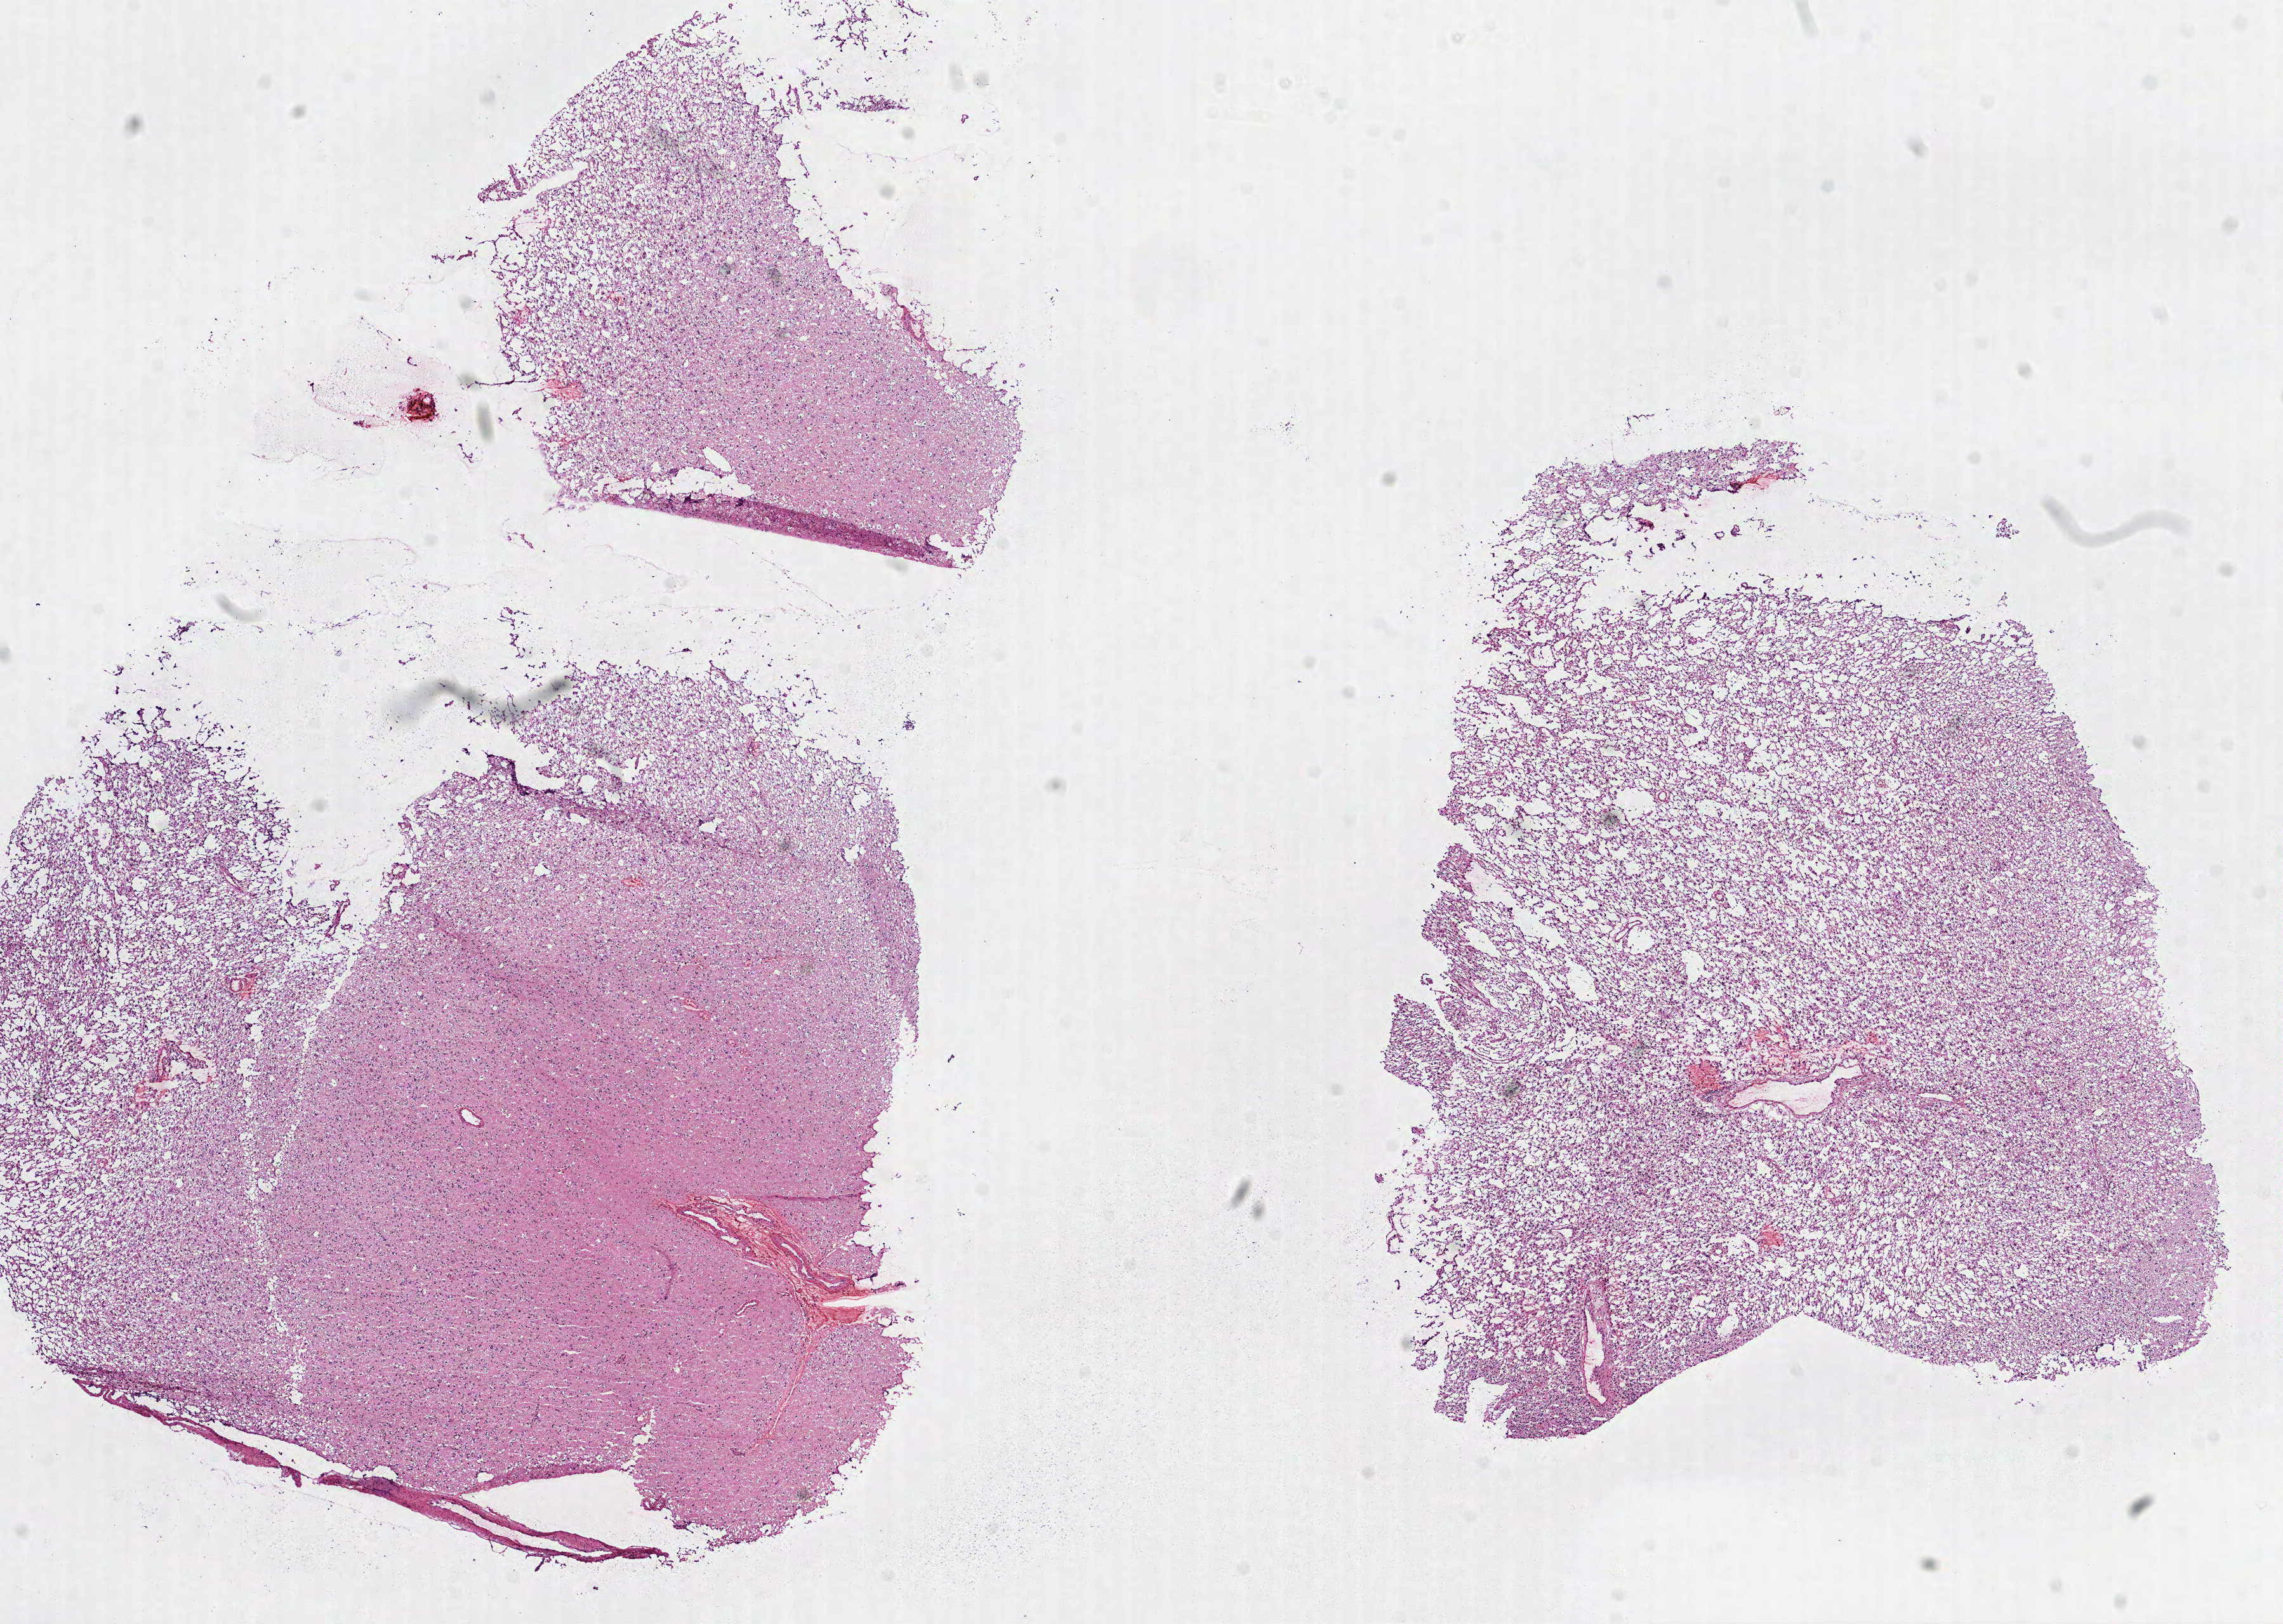
Whole-slide histology image, H&E, shown as a low-resolution overview of the whole scanned area (about 14.5 x 10.3 mm, slide scanned at 40x); frozen section from the top of the tissue portion; brain, primary tumour sample. Patient: male, age at initial diagnosis 26 years. Histologic grade: G2 (moderately differentiated). Slide review estimates, as recorded: tumour cells 100%, tumour nuclei 75%, normal cells 0%, stromal cells 0%, necrosis 0%.
• pathologic diagnosis: Astrocytoma, NOS (cerebrum)